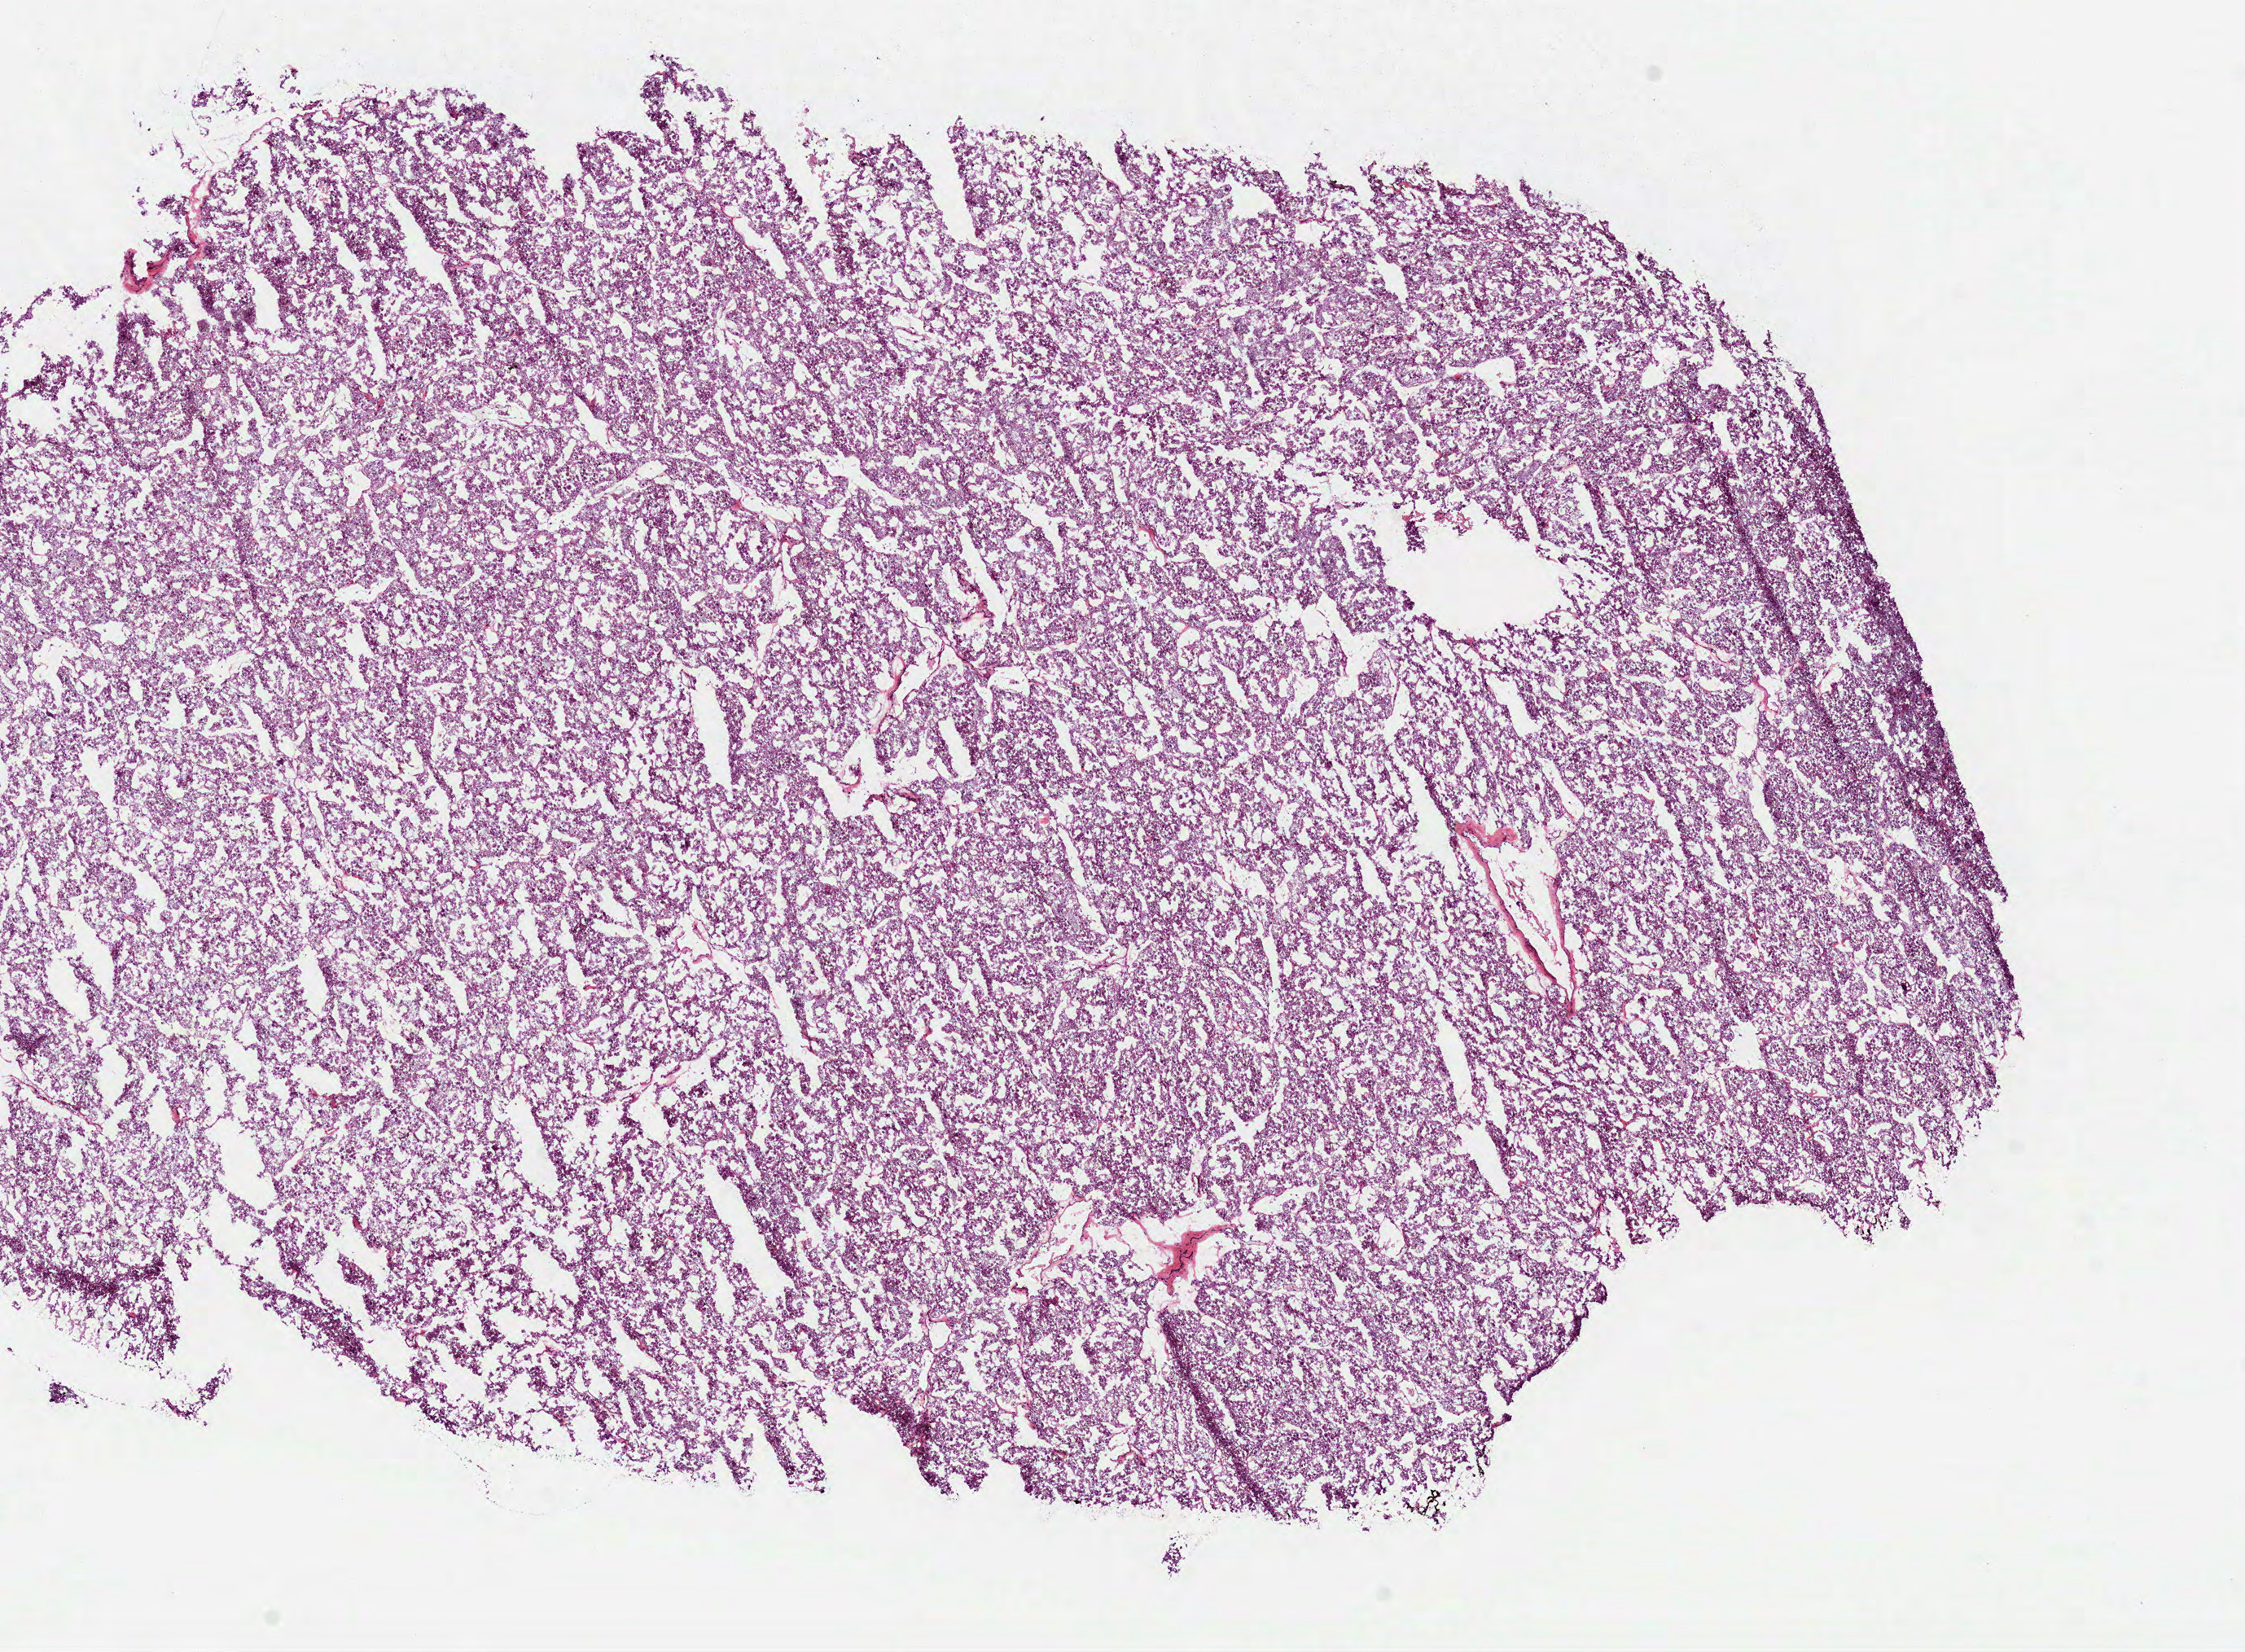
Whole-slide histology image, Hematoxylin and eosin (H&E) stained, a low-resolution overview of the entire scanned area, about 11.1 x 8.2 mm. Frozen section from the top of the tissue portion. Kidney, primary tumour sample. Female, age 40 years at initial diagnosis. Pathologist review of this section (percent, as recorded): tumour cells 82%, tumour nuclei 90%, normal cells 0%, stromal cells 15%, necrosis 3%. Inflammatory infiltration, as recorded: lymphocyte infiltration 2%, monocyte infiltration 0%, neutrophil infiltration 0%.
Diagnosis: Renal cell carcinoma, chromophobe type. AJCC pathologic stage: II.